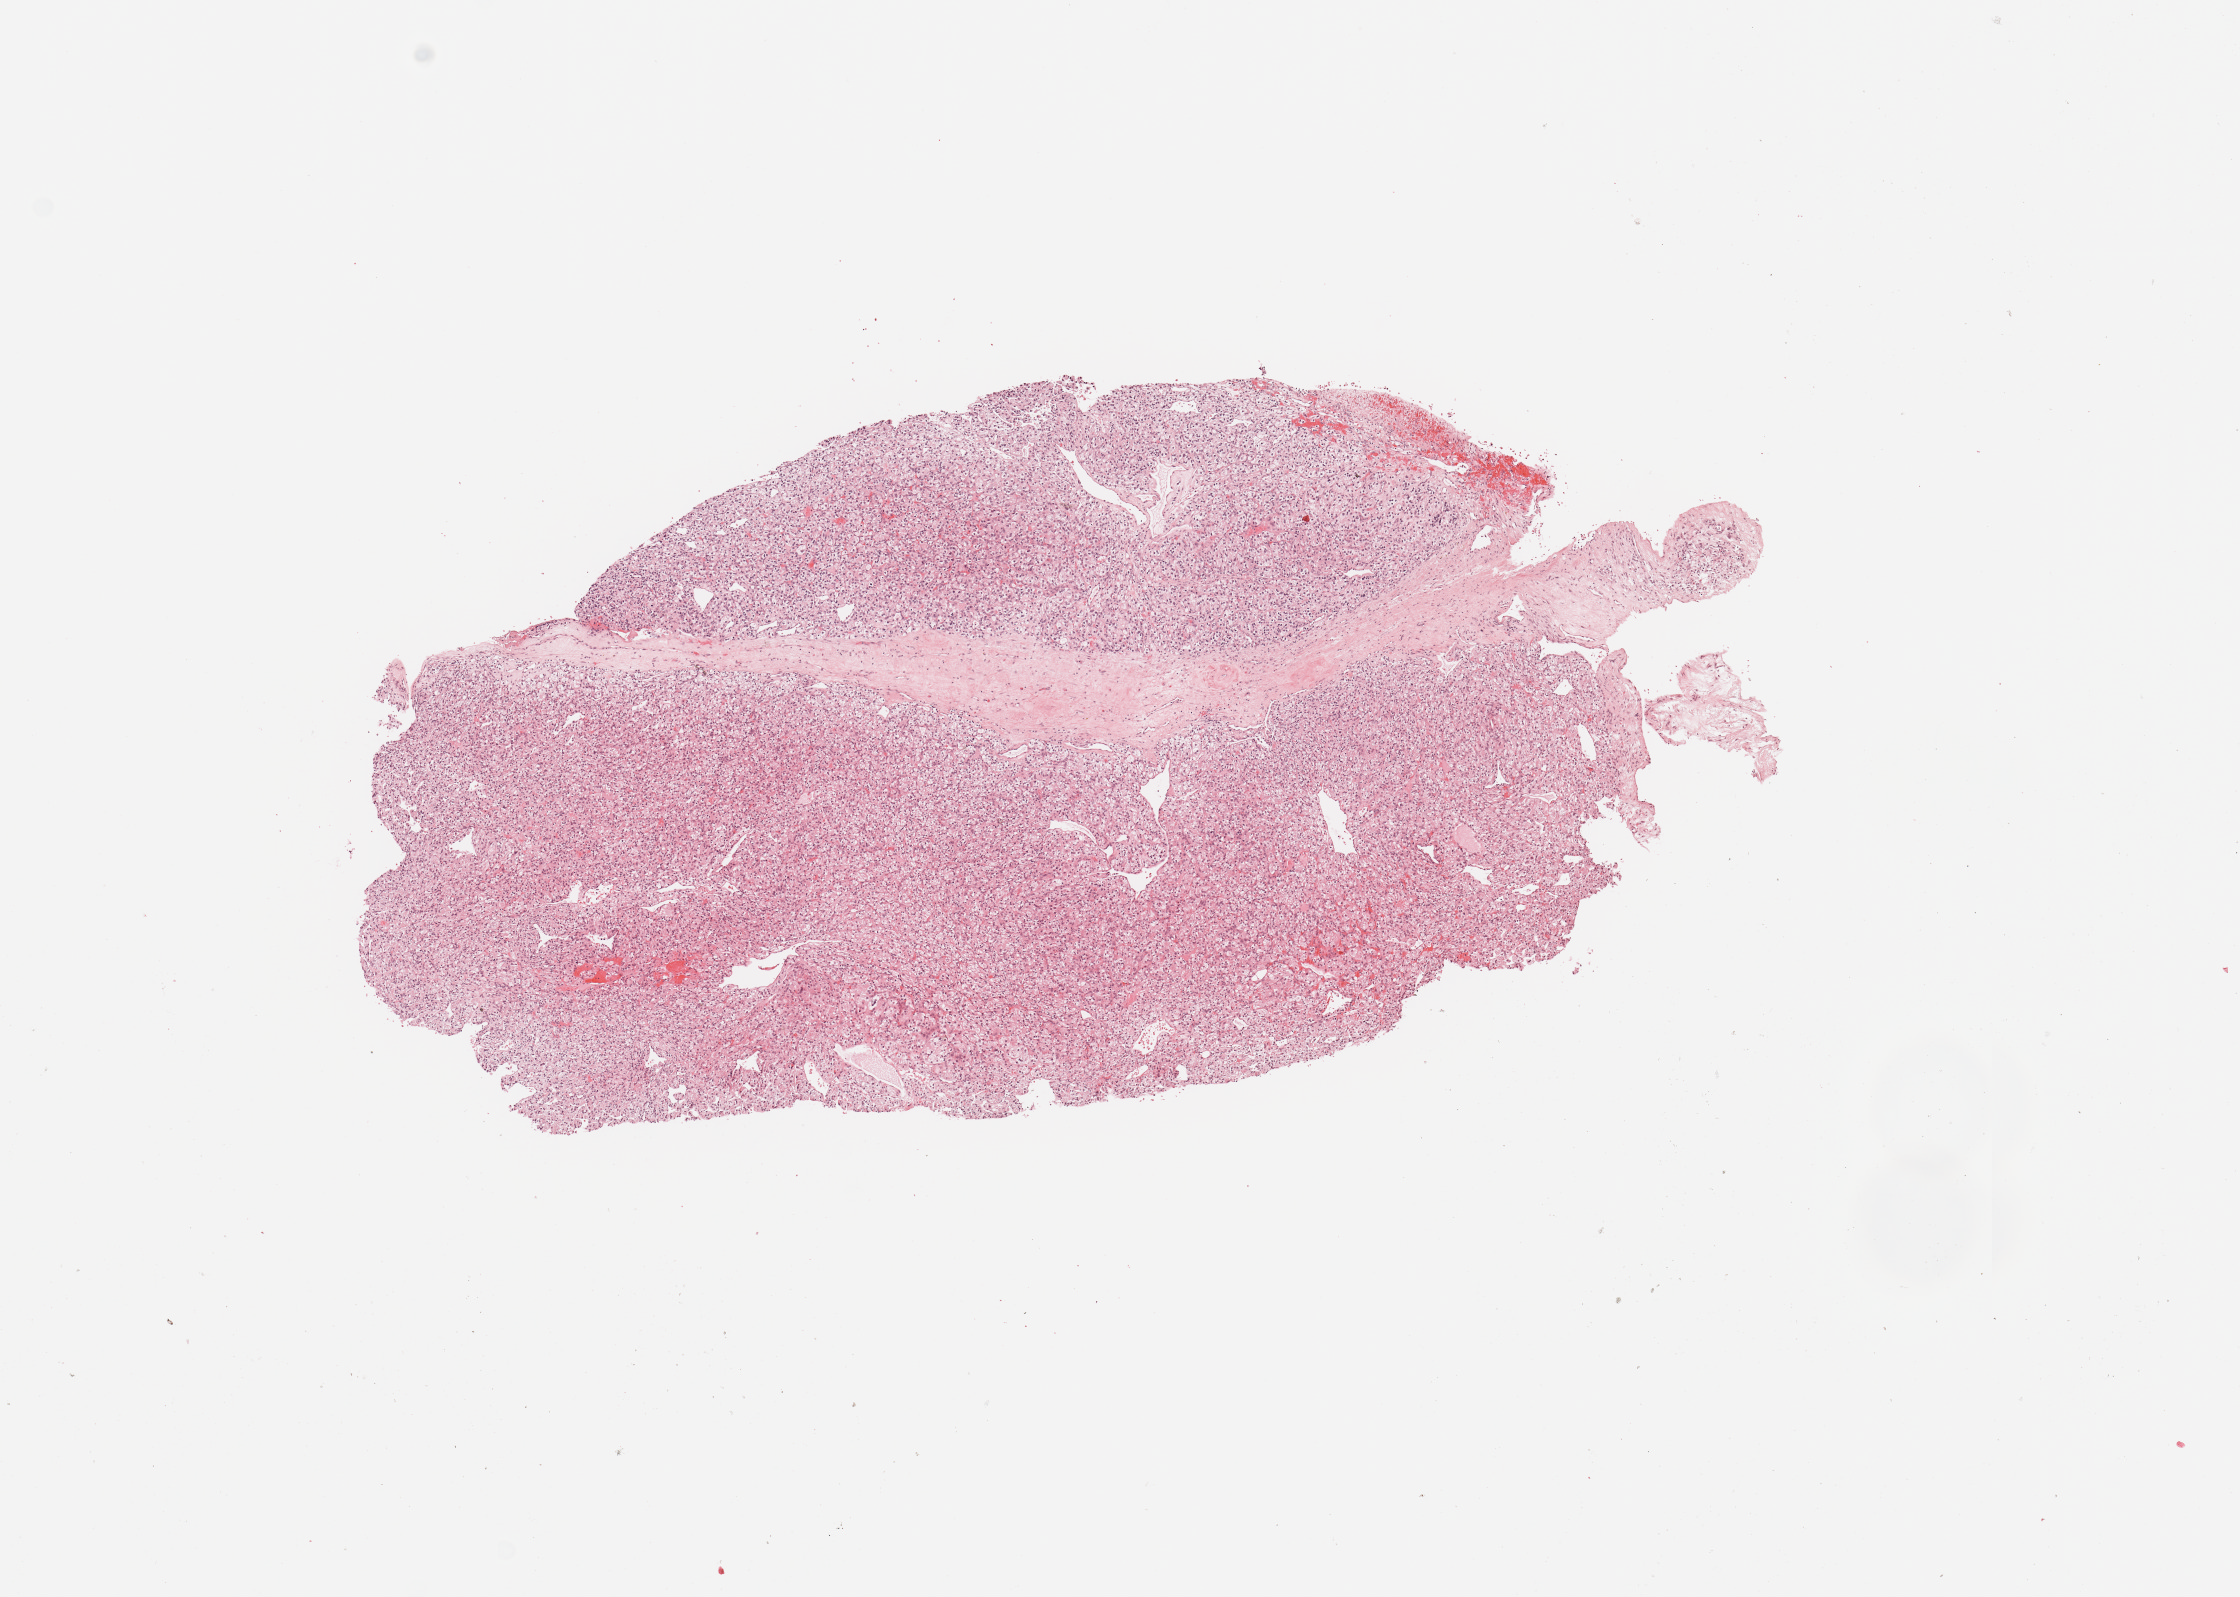
Digitized H&E tissue section (whole slide) — low-resolution overview of the scanned area, about 8.9 x 6.3 mm (from a 20x scan). Tumour tissue sample, sampled site: kidney. Patient: male, age 80 years. Histologic grade: G2 (moderately differentiated). Slide review estimates, as recorded: tumour nuclei 95%, necrosis 0%.
• diagnosis: Renal cell carcinoma, NOS
• AJCC pathologic stage: I
• primary tumour site (as recorded): lower pole